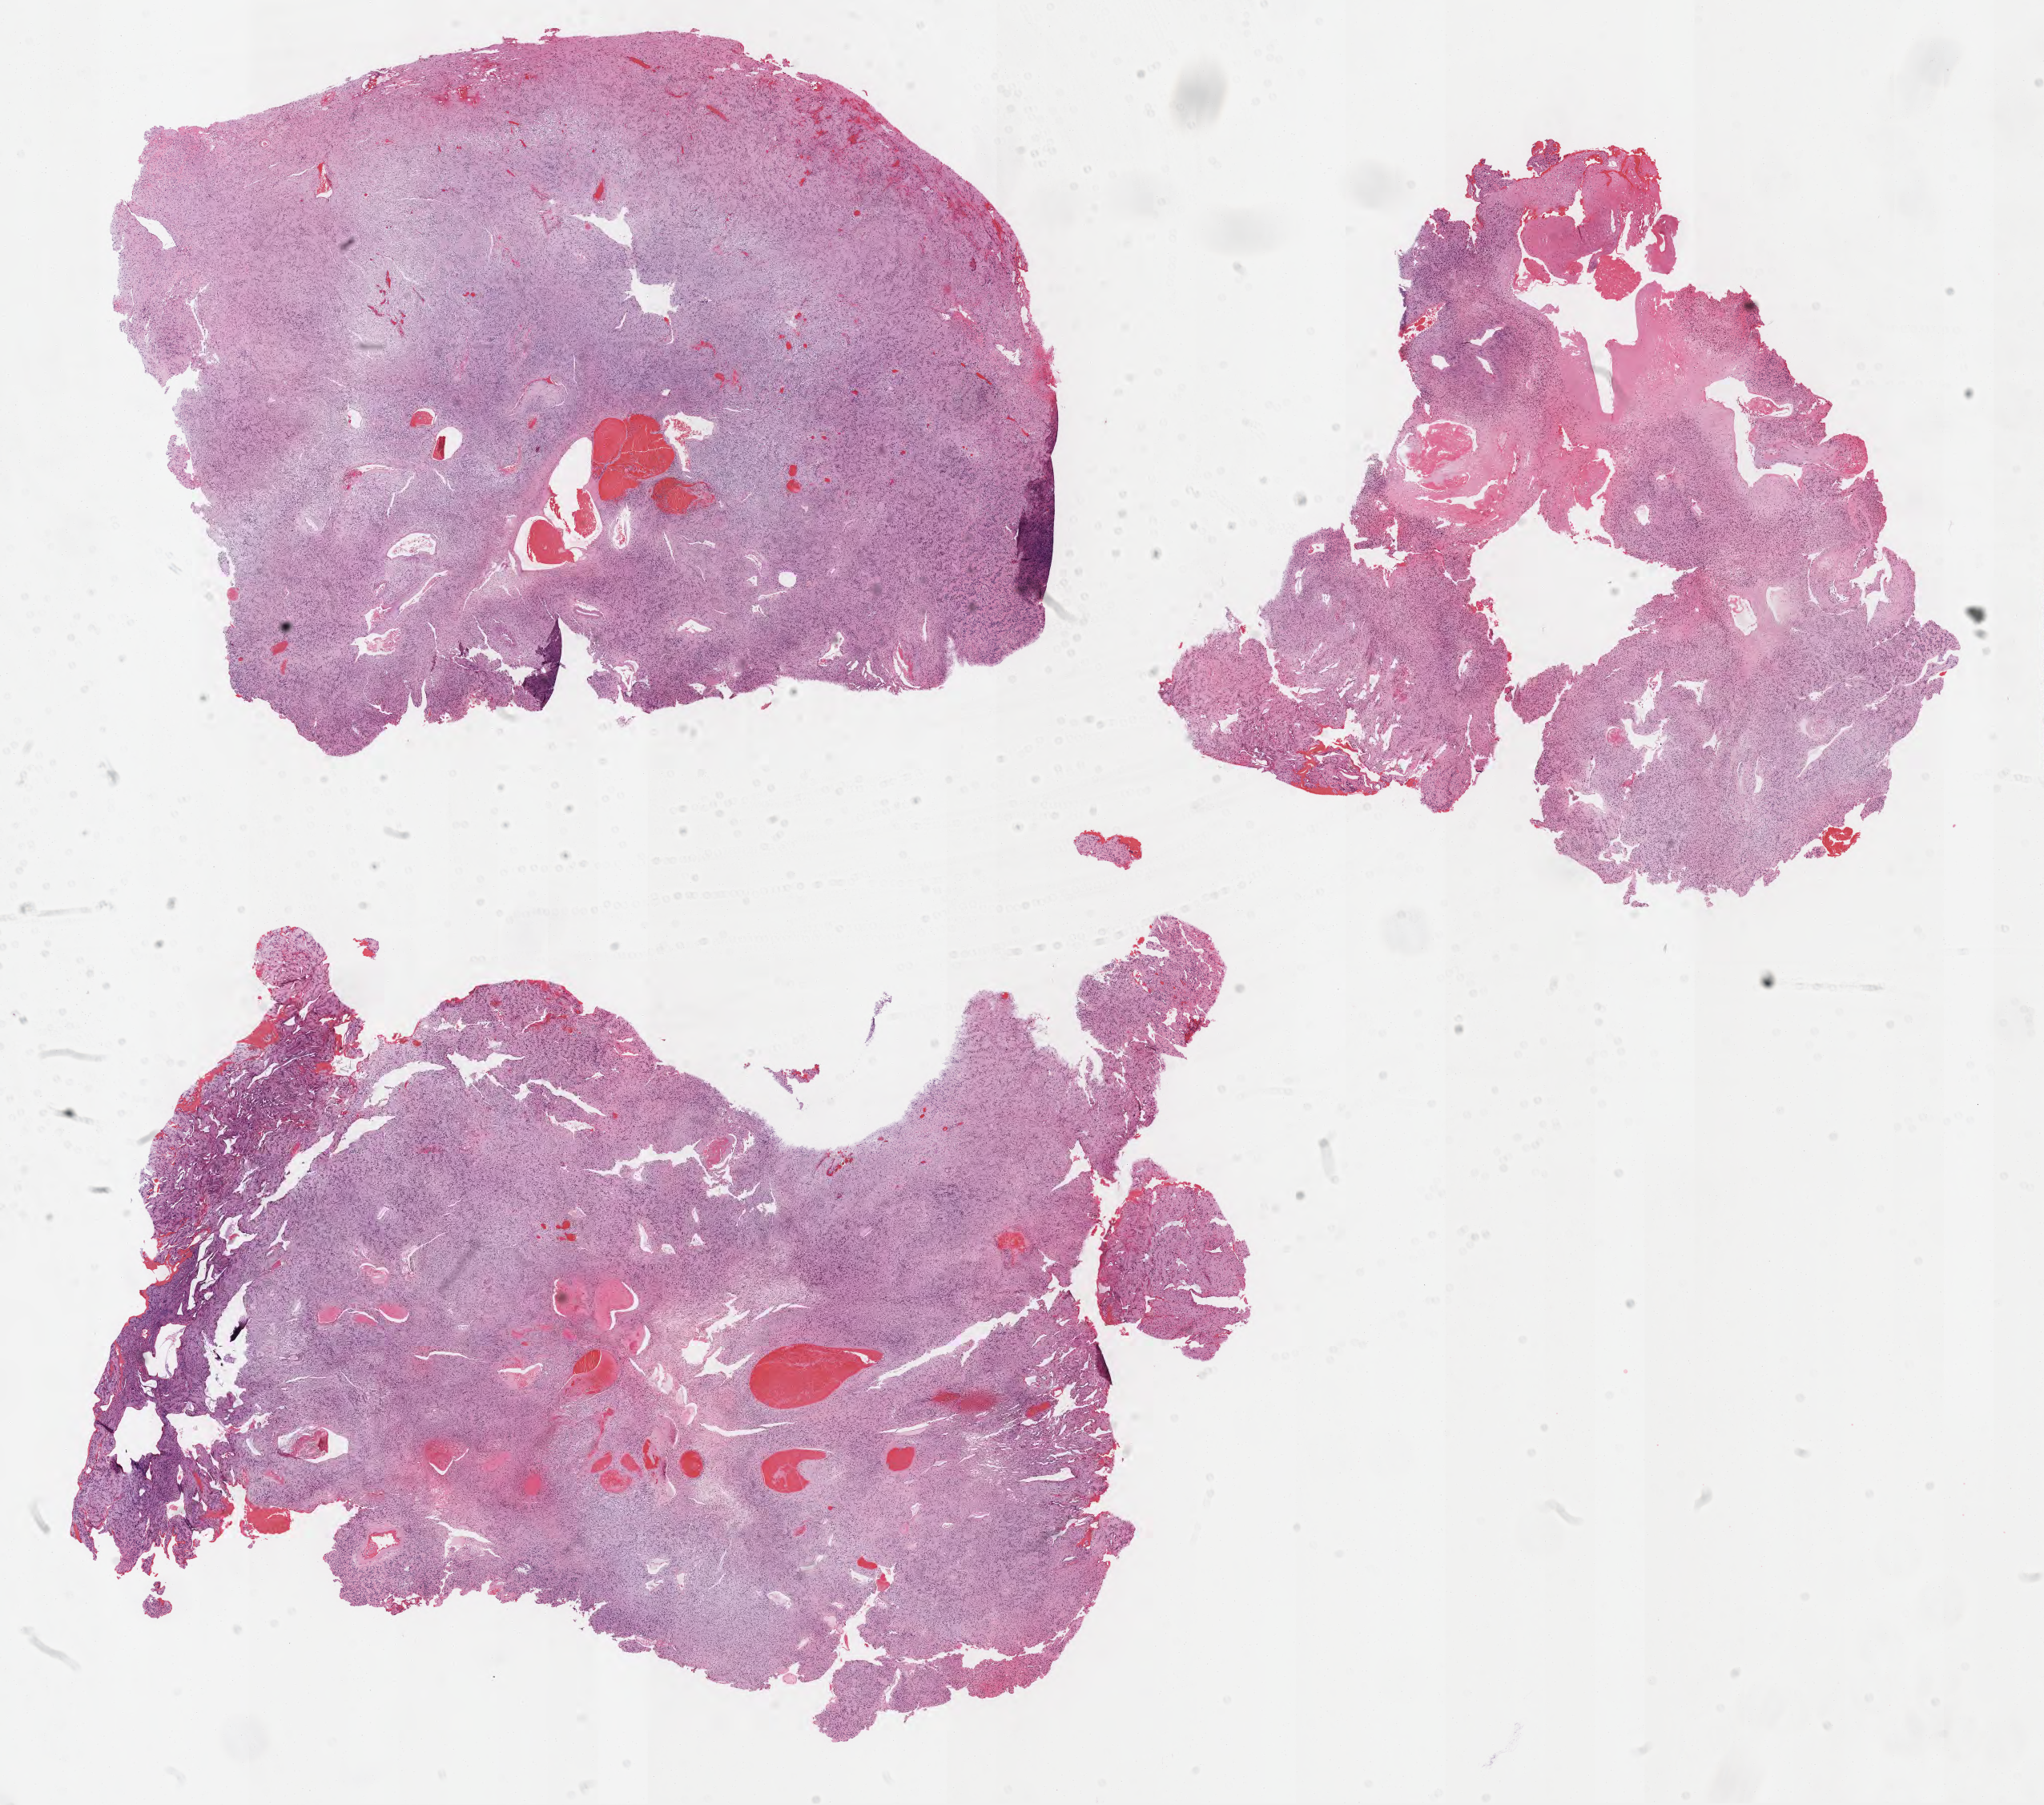
Whole-slide image, H&E stain of tumor tissue from the brain — low-resolution overview of the scanned area, about 20.6 x 18.2 mm. Formalin-fixed paraffin-embedded section. Patient male; age 106 months (8 years 10 months).
- recorded diagnosis: Schwannoma, NOS